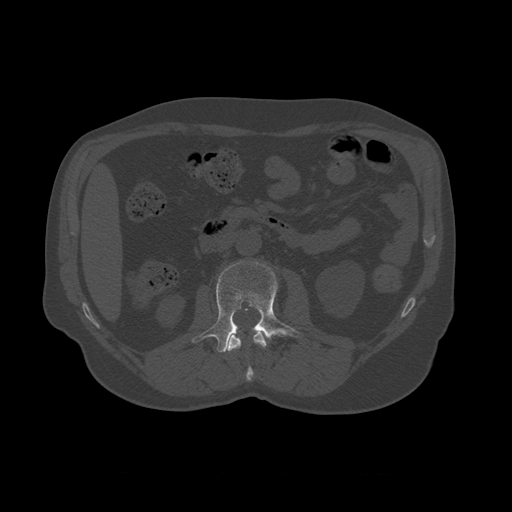
CT including the spine, one axial slice. Position 333 of 450 along the scan axis. Reconstruction kernel STANDARD. Bone window (W 1800 / L 400 HU). 1.25 mm slice thickness. 512 × 512 image matrix, field of view 405 × 405 mm. Patient age 75 years. From the clinical record (not read from this slice): primary cancer: prostate.
Annotated regions visible in this slice (semi-automatically segmented with operator editing):
- L1 vertebra: bounding box (x1, y1, x2, y2) in pixels: (226, 331, 268, 381)
- L2 vertebra: (192, 261, 301, 353)